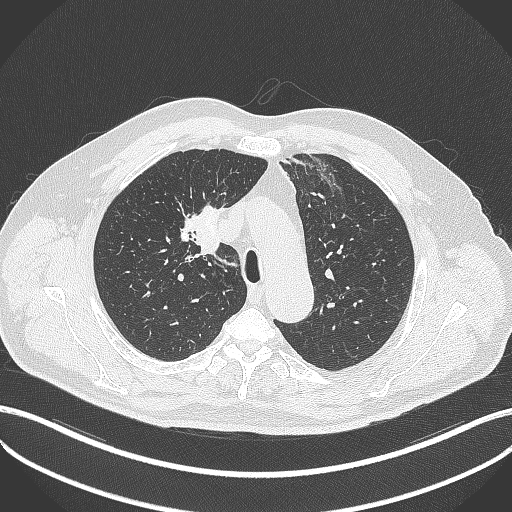
Chest CT, one axial slice; slice 288 of 411 in the series (ordered by position); lung window (W 1500 / L -600 HU); 1 mm slice thickness; 512 × 512 image matrix, field of view 400 × 400 mm. Male patient, age 60 years. From the clinical record (not read from this slice): clinical TNM (as recorded): T1b N1 M0.
Annotated regions visible in this slice (bounding box drawn by a radiologist):
- lung tumour (recorded histology: squamous cell carcinoma): bounding box [x1, y1, x2, y2] px = [183, 198, 223, 258]